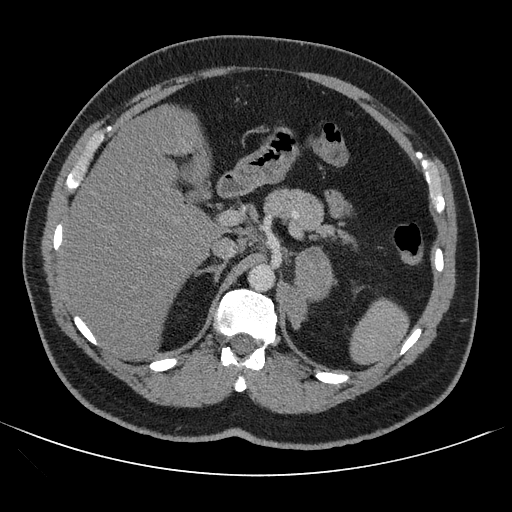
Contrast-enhanced abdominal CT, one axial slice; slice 69 of 121 in the series (ordered by position); soft-tissue window (W 400 / L 40 HU); 2.5 mm slice thickness; 512 × 512 image matrix, field of view 399 × 399 mm. Patient: male, 53 years. Case-level facts recorded for this patient, not image findings: diagnosis: adrenocortical carcinoma; tumour side: left adrenal.
Outlined on this slice (semi-automatic segmentation, software-assisted and operator-edited):
- mass: bounding box [x1, y1, x2, y2] px = [287, 249, 332, 329]